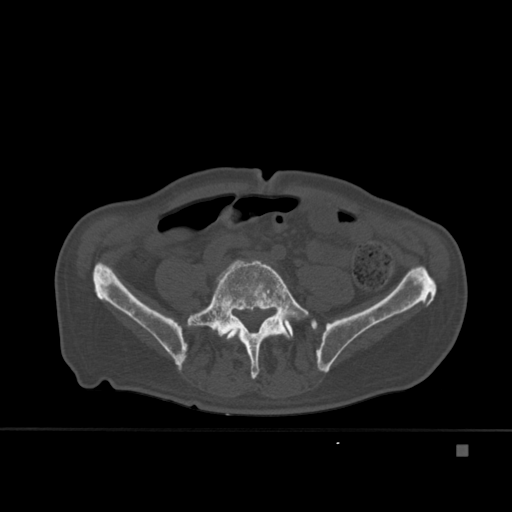
CT including the spine, one axial slice; position 105 of 451 along the scan axis; bone window (W 1800 / L 400 HU); 512 × 512 image matrix, field of view 378 × 378 mm. Male patient, age 75 years. From the clinical record (not read from this slice): primary cancer: prostate.
Structures marked on this image (semi-automatically segmented with operator editing):
- L4 vertebra: bounding box [x1, y1, x2, y2] px = [225, 330, 235, 340]
- L5 vertebra: [186, 260, 309, 379]
- T7 vertebra: [210, 300, 239, 320]